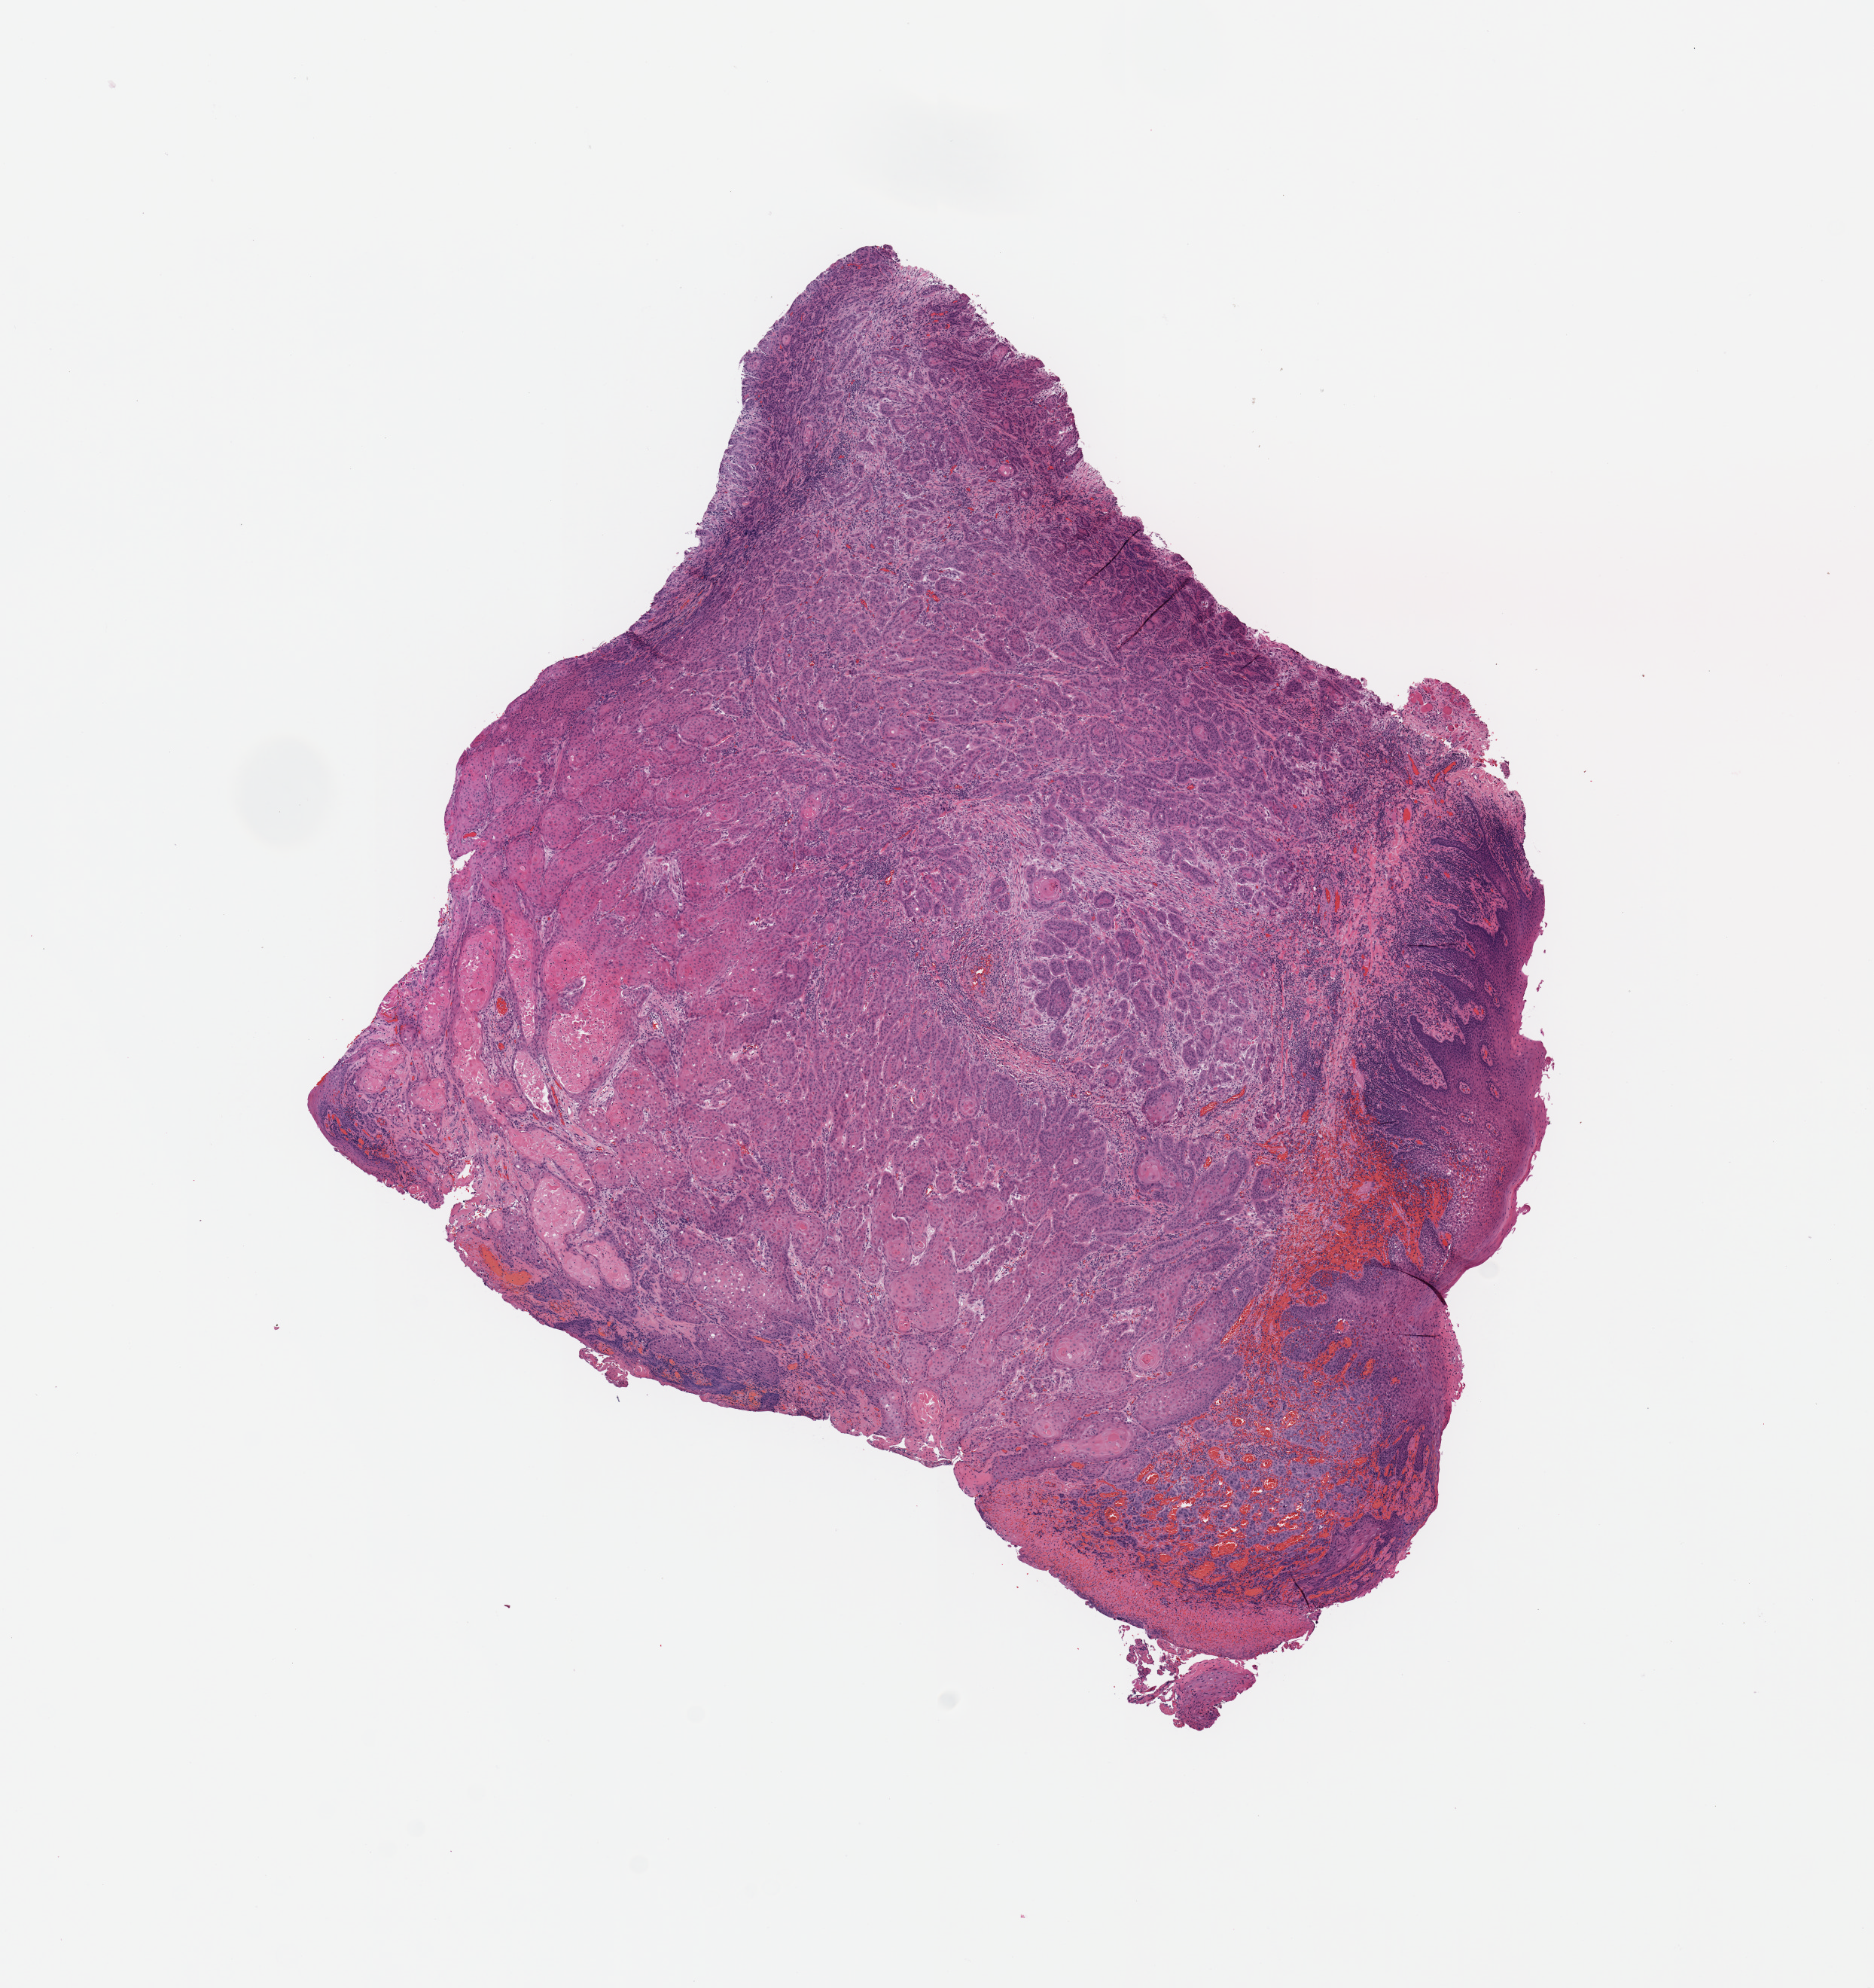
Digitized Hematoxylin and eosin (H&E) stained tissue section (whole slide), whole scanned area (about 9.8 x 10.4 mm, from a 20x scan) shown as a low-resolution overview. Tumour tissue sample, sampled site: floor of mouth. Male, 56 y/o. Histologic grade: G1 (well differentiated). Composition of this section per pathologist review: tumour nuclei 85%, necrosis 3%.
Primary tumour site (as recorded): oral cavity. AJCC pathologic stage: II. Histologic diagnosis: Squamous cell carcinoma, NOS (floor of mouth, NOS).